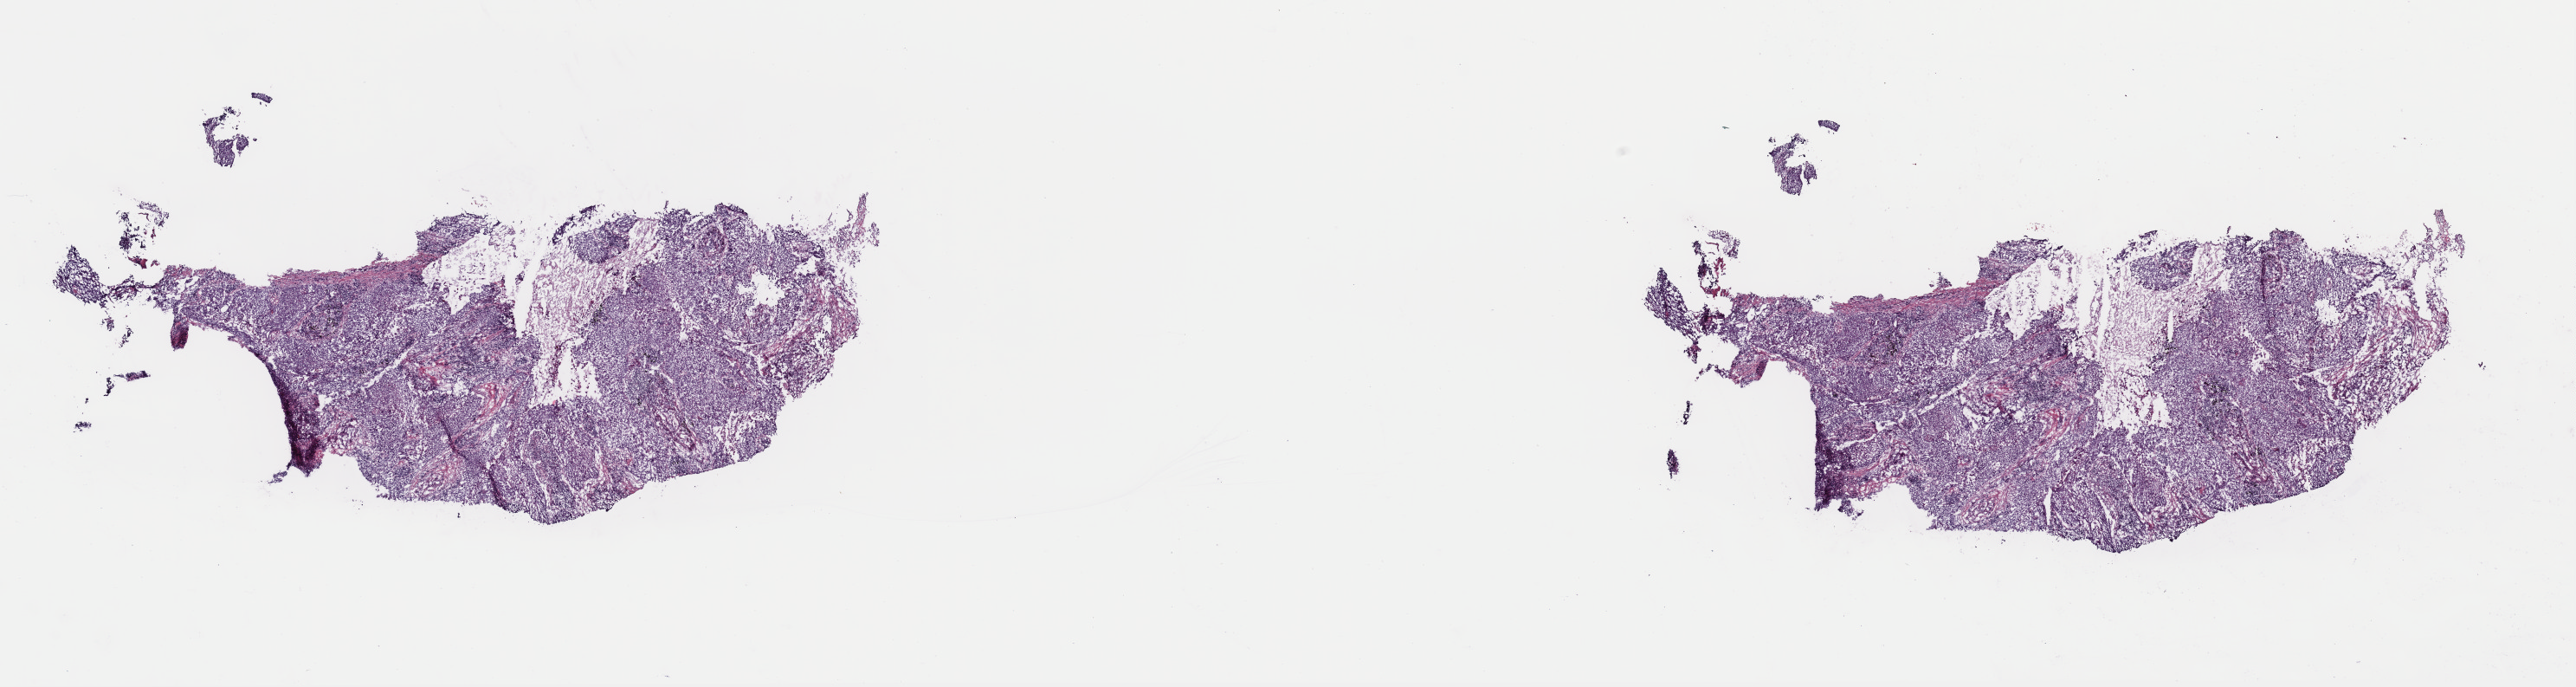
Whole-slide histology image, Hematoxylin and eosin (H&E) stained — shown as a low-resolution overview of the whole scanned area (about 23.5 x 6.3 mm), frozen section, sample: primary tumour, lung. Male patient; age at initial diagnosis 60 years. Slide review estimates, as recorded: tumour cells 80%, tumour nuclei 90%, normal cells 10%, stromal cells 10%, necrosis 0%. Inflammatory infiltration, as recorded: lymphocyte infiltration 0%, monocyte infiltration 0%, neutrophil infiltration 0%.
- TNM: T2a N0 MX
- AJCC pathologic stage: IB
- diagnosis: Squamous cell carcinoma, NOS